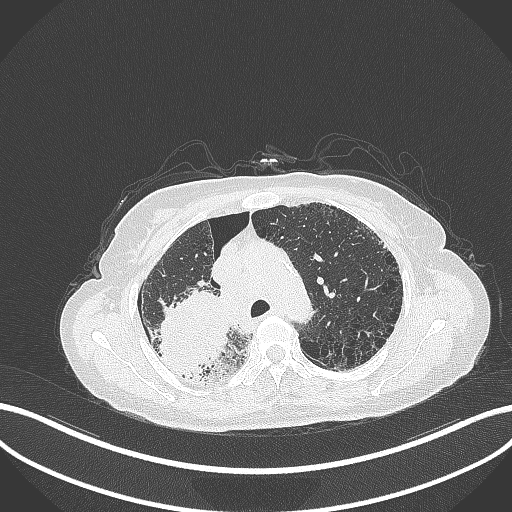
Chest CT, one axial slice; slice 252 of 408 in the series (ordered by position); 120 kVp; lung window (W 1500 / L -600 HU); 1 mm slice thickness; 512 × 512 image matrix, field of view 400 × 400 mm. Patient: female, 64 years. From the clinical record (not read from this slice): clinical TNM (as recorded): T3 N3 M0.
Structures marked on this image (bounding box drawn by a radiologist):
- lung tumour (recorded histology: squamous cell carcinoma): bounding box <155,290,231,382> (left, top, right, bottom; pixels)